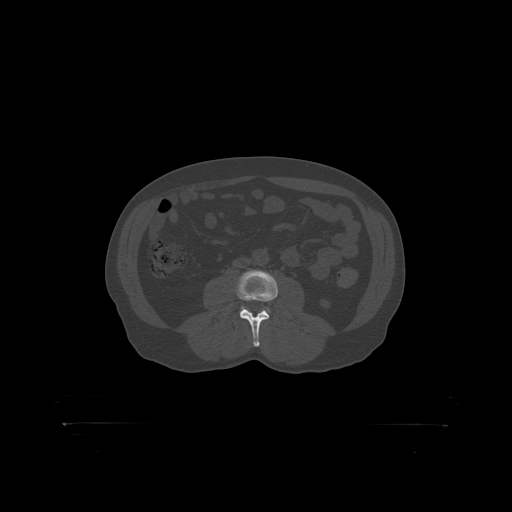
CT including the spine, one axial slice; slice 258 of 399 in the series (ordered by position); reconstruction kernel STANDARD; bone window (W 1800 / L 400 HU); 1.25 mm slice thickness; 512 × 512 image matrix, field of view 650 × 650 mm. Patient: male, 46 years. Case-level facts recorded for this patient, not image findings: primary cancer: skin.
Structures marked on this image (semi-automatic segmentation, software-assisted and operator-edited):
- L3 vertebra: bounding box [x1, y1, x2, y2] px = [236, 271, 278, 319]
- L4 vertebra: [242, 308, 271, 313]